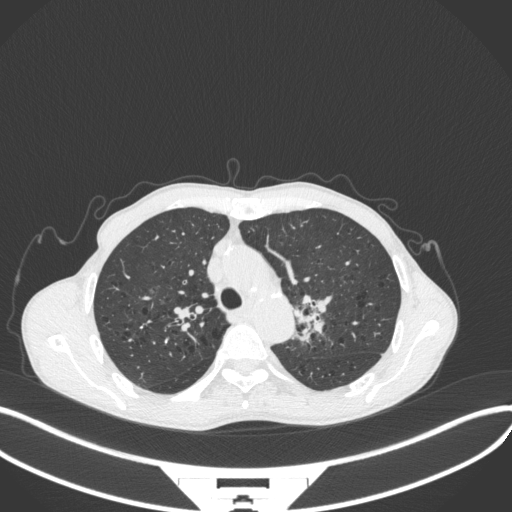
Chest CT, one axial slice. Slice 304 of 394 in the series (ordered by position). Reconstruction kernel B31f. Lung window (W 1500 / L -600 HU). 512 × 512 image matrix, field of view 400 × 400 mm. Patient: male, 65 years. From the clinical record (not read from this slice): clinical TNM (as recorded): T2b N0 M0.
Outlined on this slice (bounding box drawn by a radiologist):
- lung tumour (recorded histology: adenocarcinoma): bounding box (x1, y1, x2, y2) in pixels: (293, 288, 337, 343)